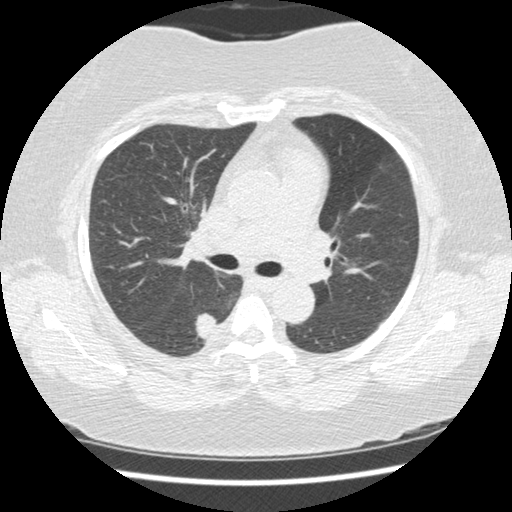
Chest CT (low-dose screening protocol), one axial image, second annual screen, lung window (W 1500 / L -600 HU), 1.25 mm slice thickness, 512 × 512 image matrix. Female, age 58 years at enrolment. Current smoker at enrolment.
Expert-annotated lung lesion, bounding box (x1, y1, x2, y2) in pixels: (189, 308, 229, 354). The exam's reader record, not a measurement of the box and not confirmed to be the same lesion: non-calcified nodule or mass ≥4 mm, right lower lobe, 15 × 15 mm, spiculated (stellate) margins, soft tissue attenuation, pre-existing on the prior screen: yes; interval growth: yes. Participant outcome: lung cancer diagnosed 21 days after this screen — adenocarcinoma, NOS, right lower lobe, stage IB (AJCC 6th edition), 15 mm at pathology.